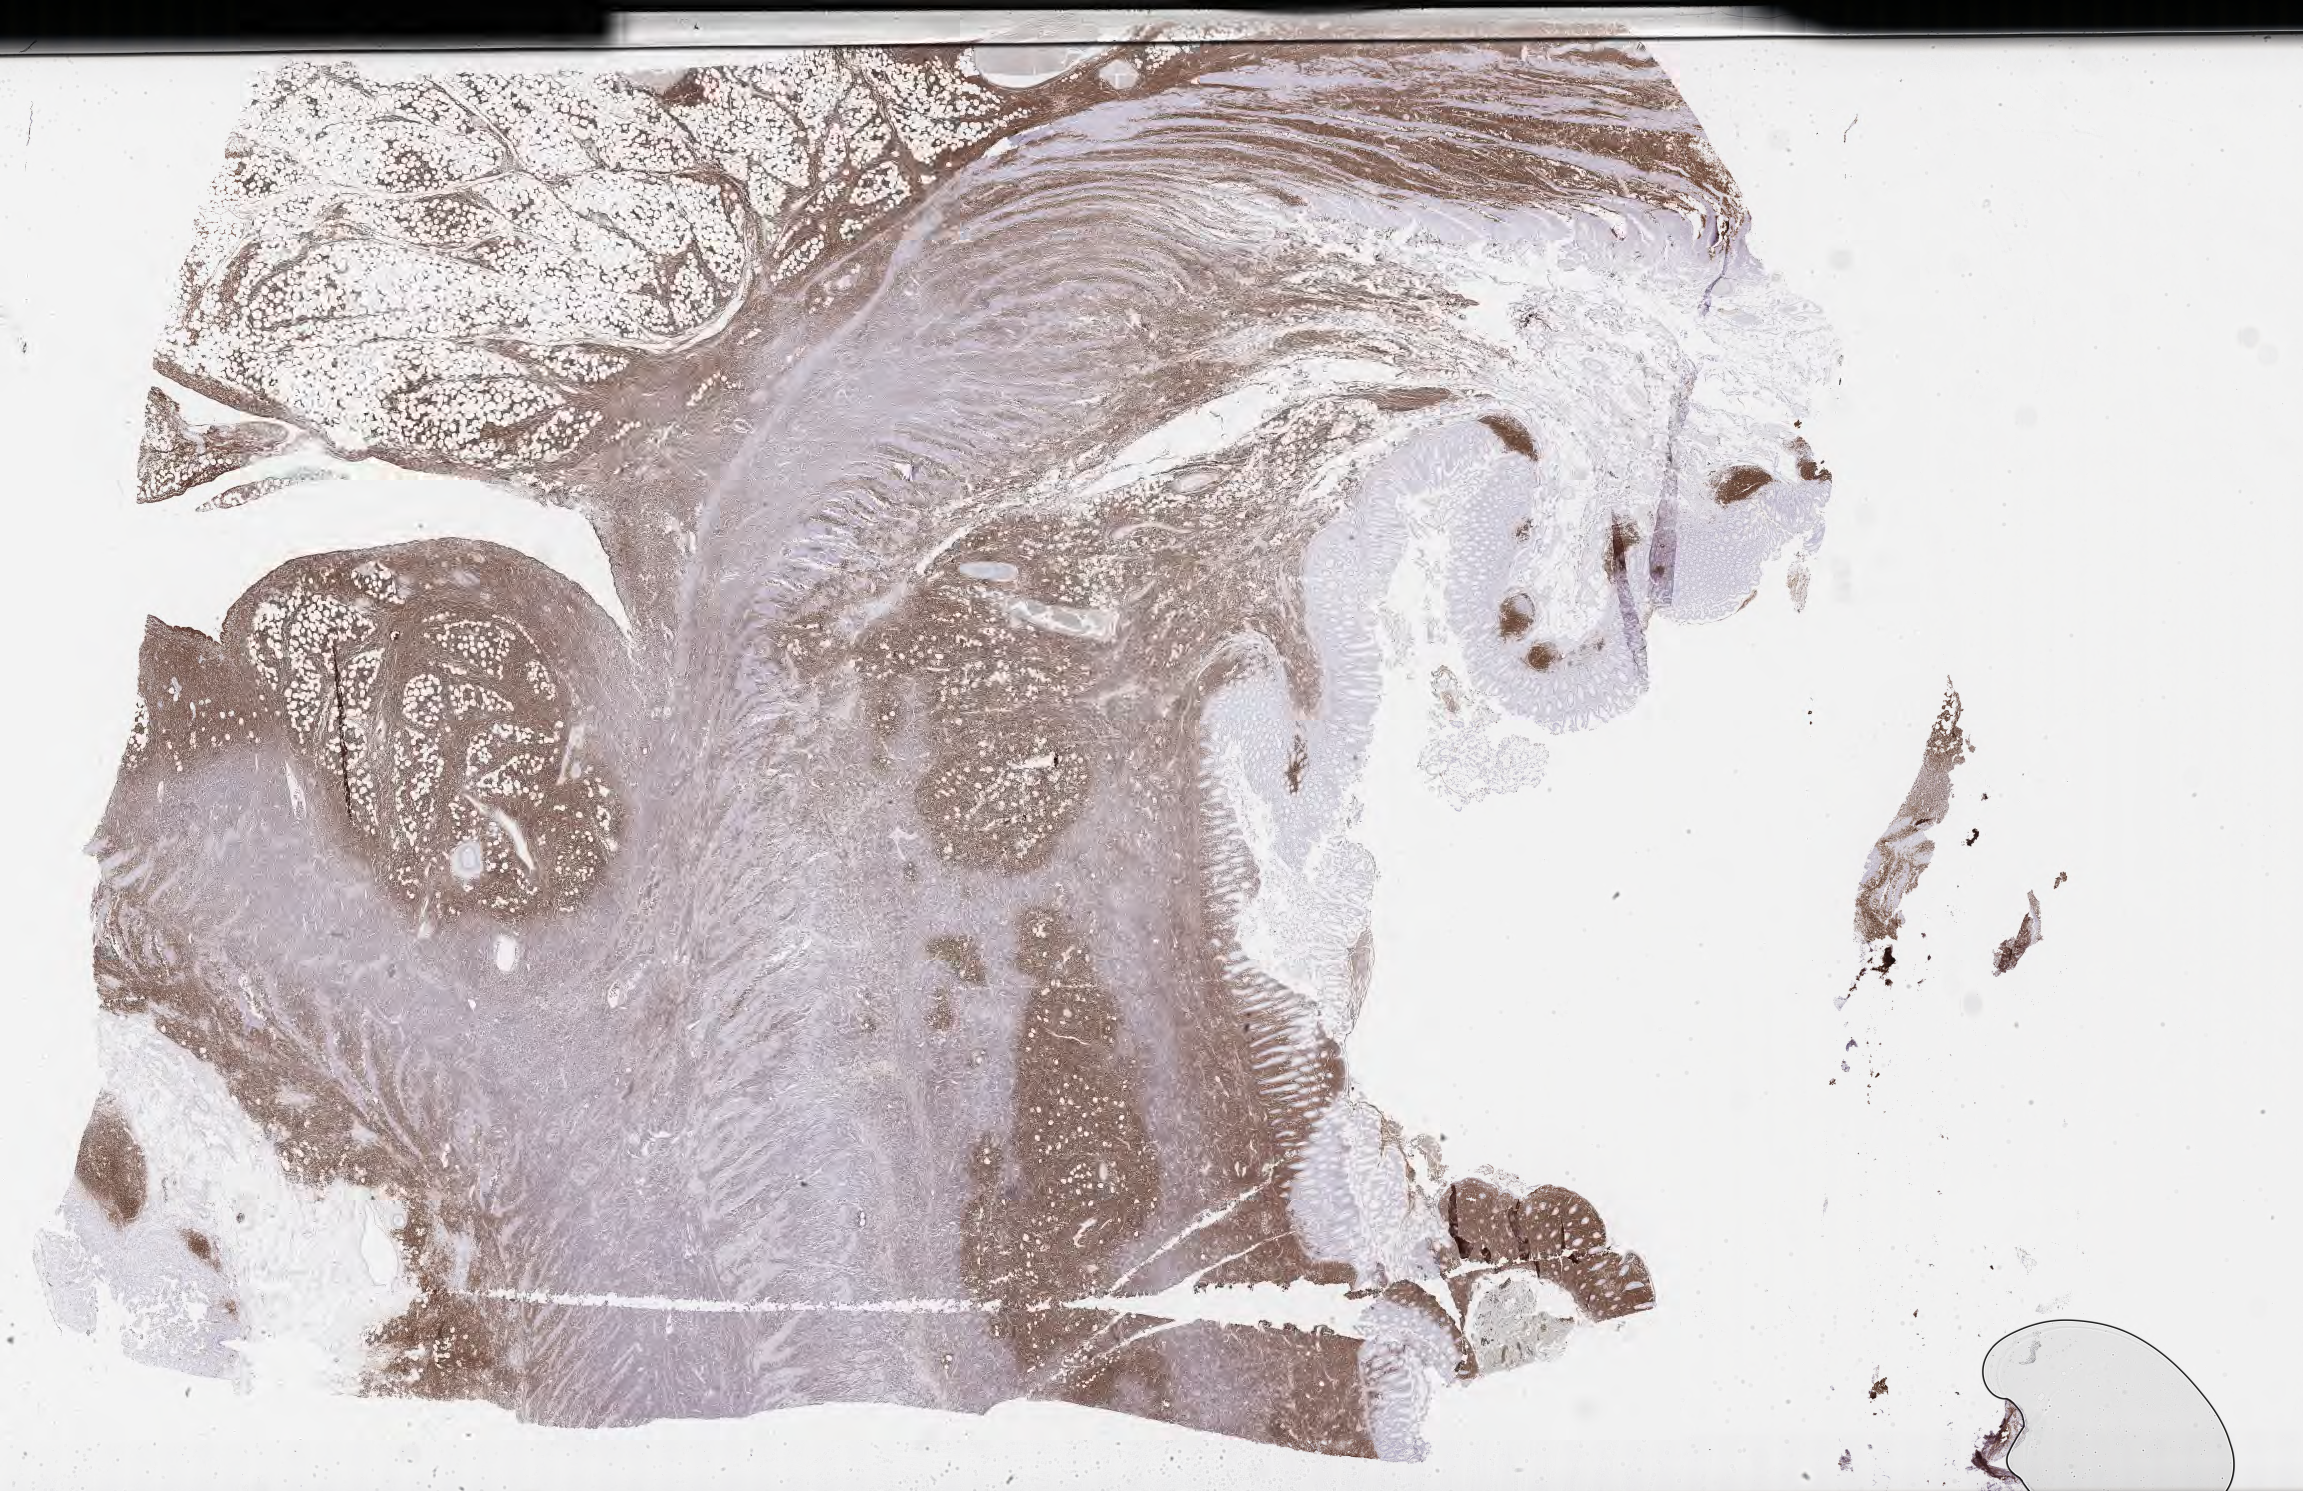
IHC for CD20, whole-slide image — a low-resolution overview of the entire scanned area, about 37.2 x 24.1 mm; specimen: tumor tissue. Patient: male, 56 years old.
* histologic diagnosis: Burkitt lymphoma, NOS